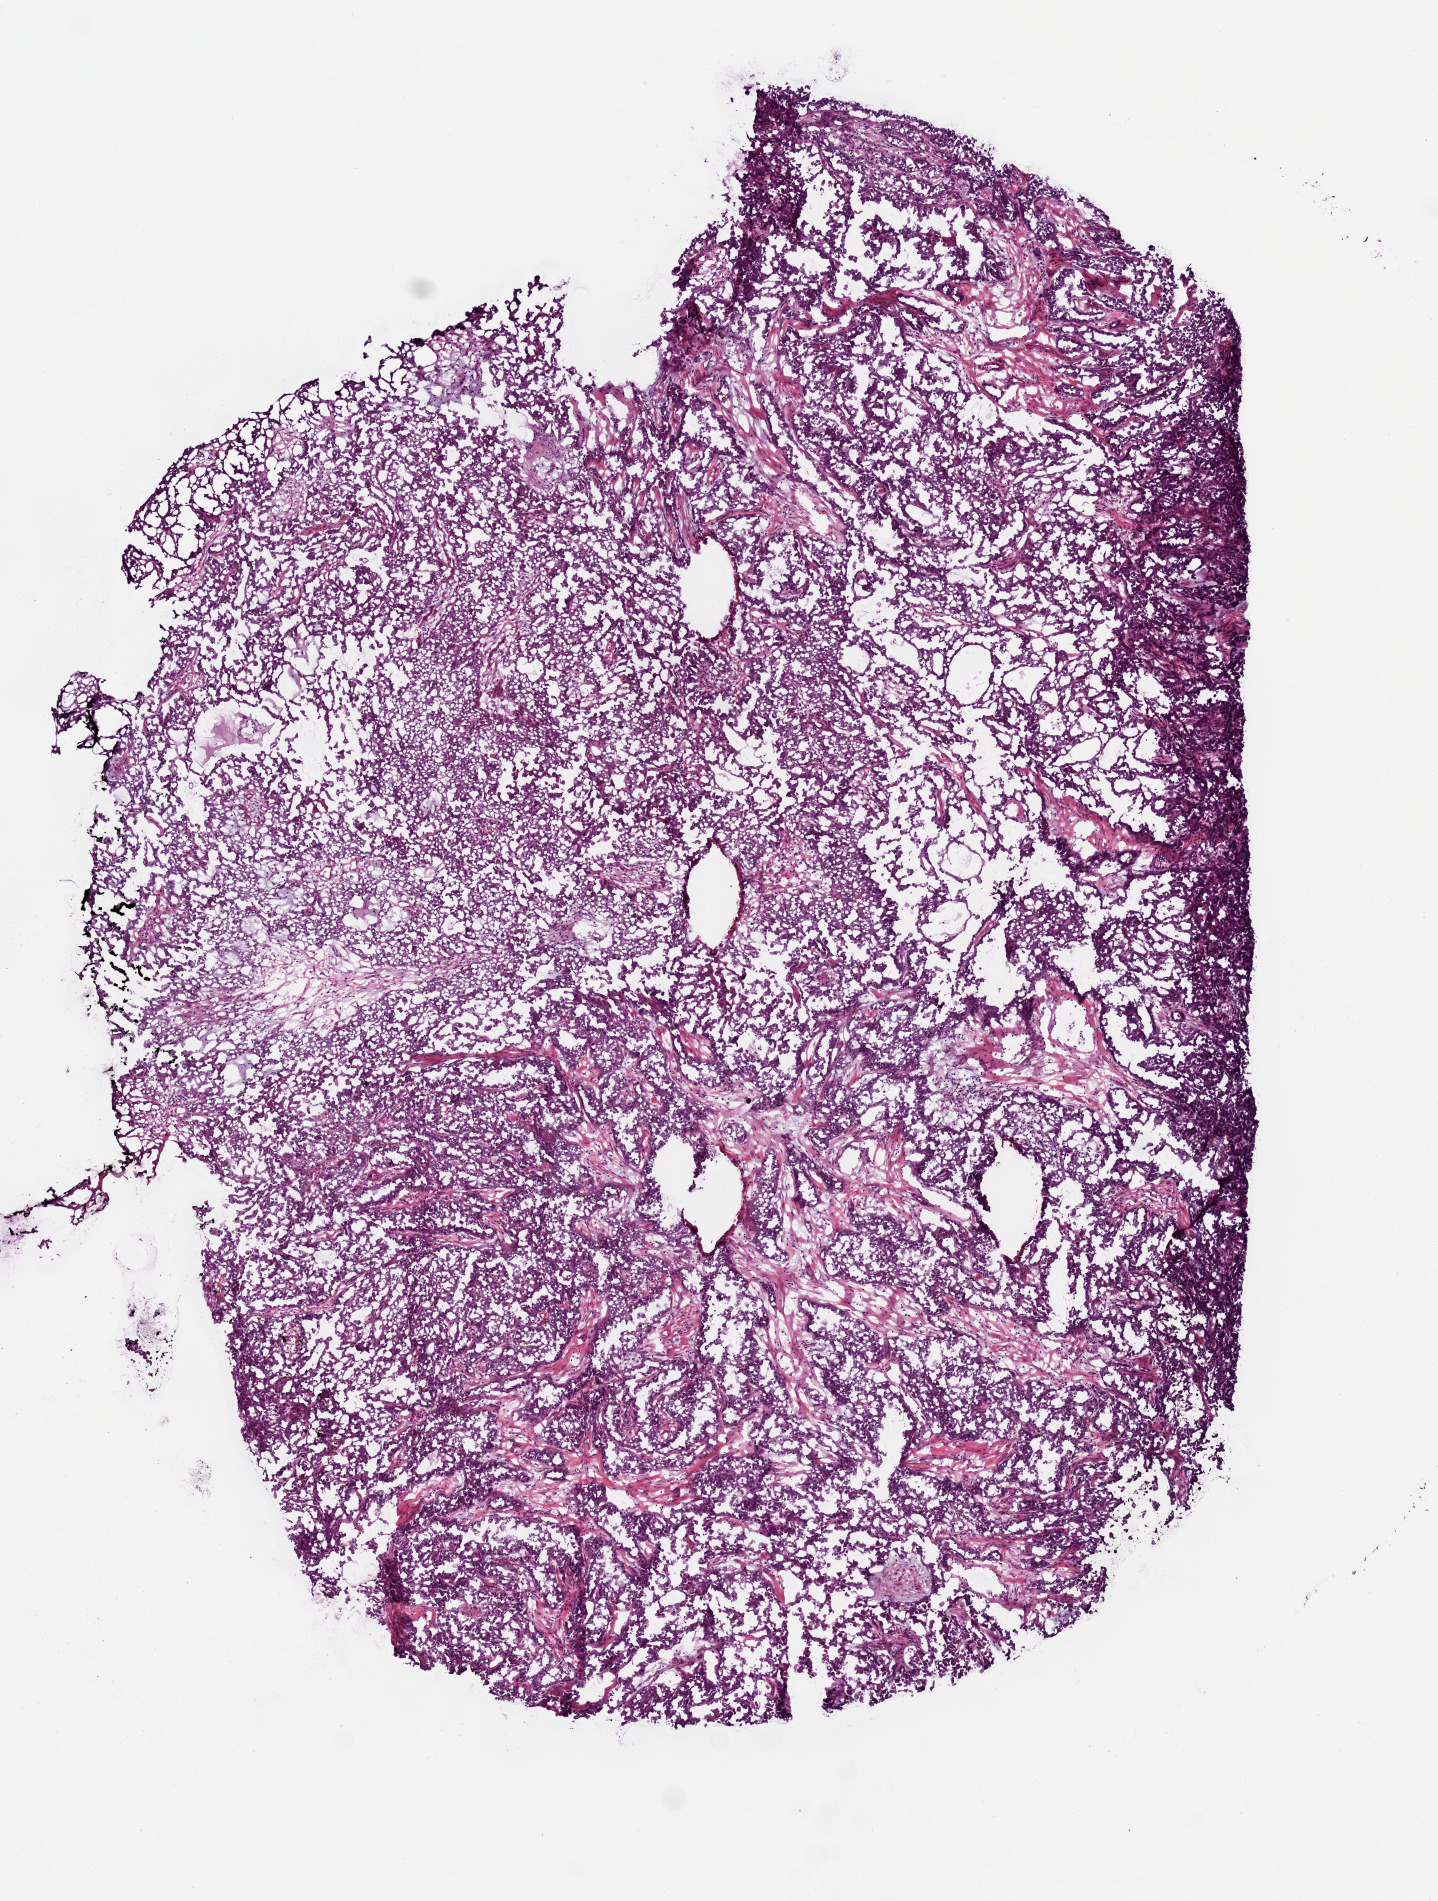
Digitized H&E tissue section (whole slide), whole scanned area (about 5.8 x 7.7 mm) shown as a low-resolution overview; frozen section from the top of the tissue portion; primary tumour sample from the kidney. Female patient; age at initial diagnosis 35 years. Slide review estimates, as recorded: tumour nuclei 75%, necrosis 0%.
* AJCC pathologic stage: II (7th edition)
* lymph nodes positive (case pathology): 0 of 2 examined
* histologic diagnosis: Papillary adenocarcinoma, NOS